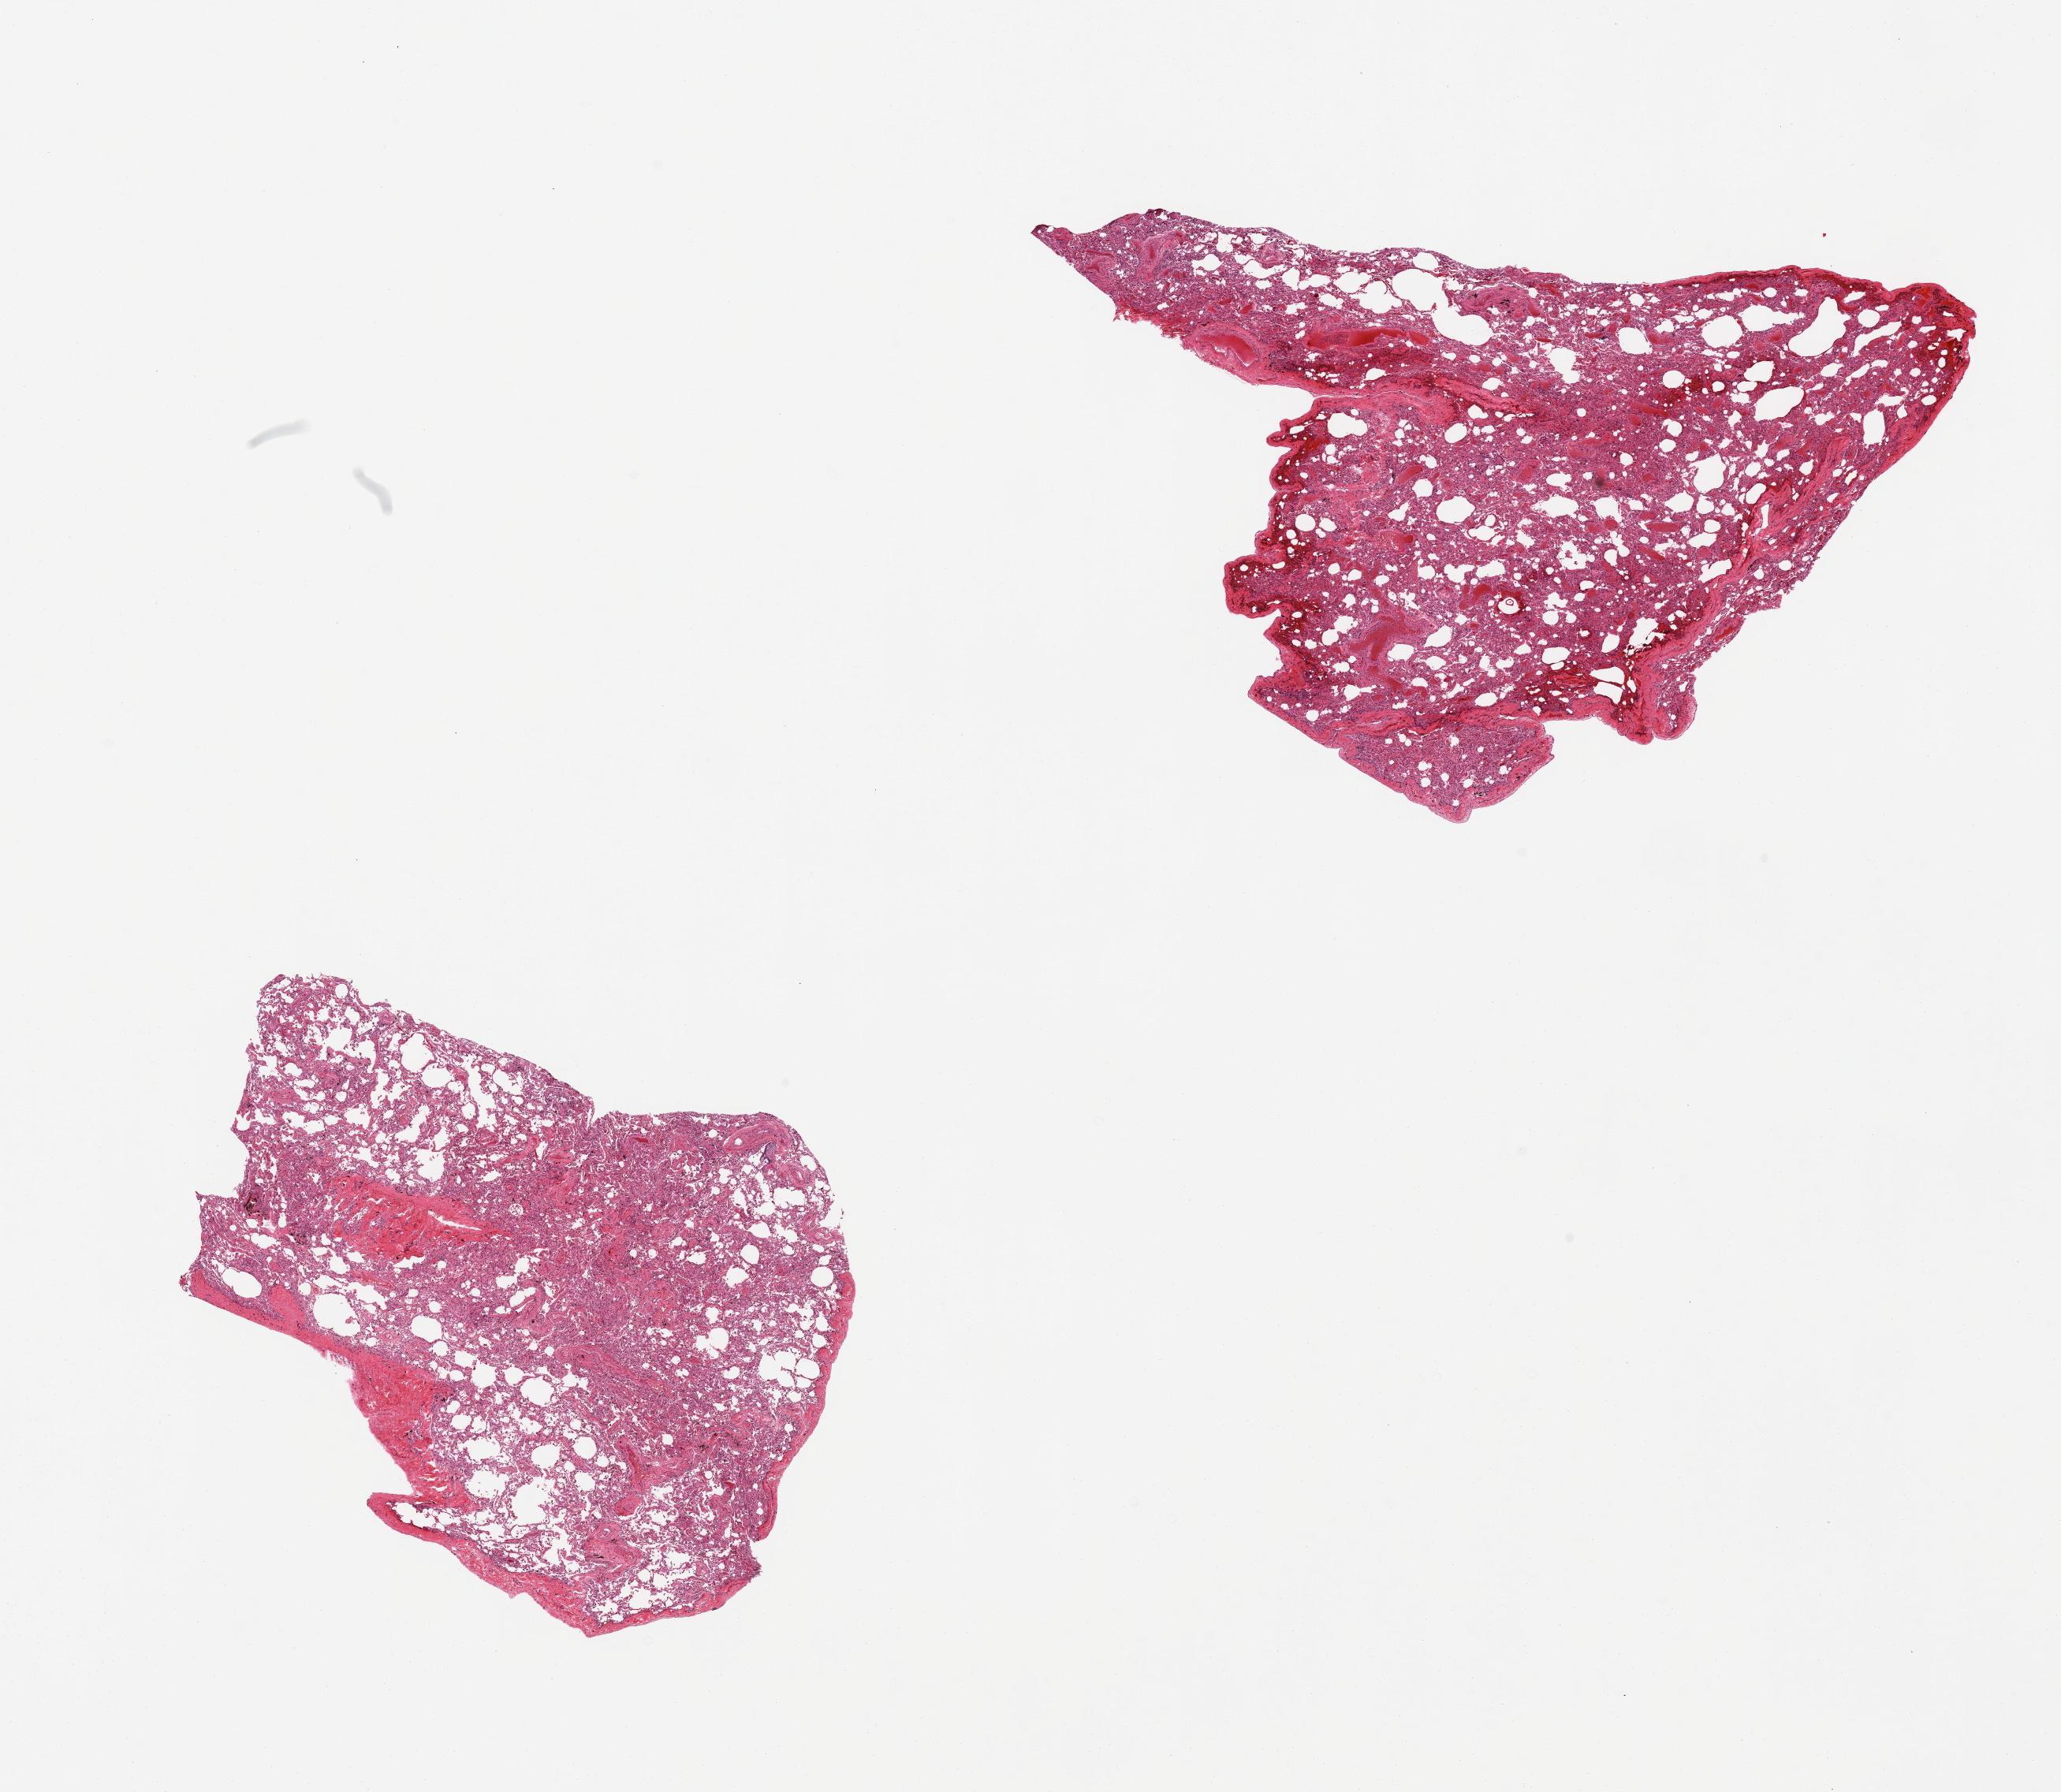
Whole-slide image, H&E stain — low-resolution overview of the scanned area, about 20.7 x 18.0 mm (from a 20x scan); PAXgene-fixed, paraffin-embedded tissue; target tissue: lung; donor tissue sample. Donor: male.
Reviewer comment on this tissue sample: 2 pieces, includes pleura (target is 1 cm below pleura), numerous hemosiderin-laden macrophages, some congestion.